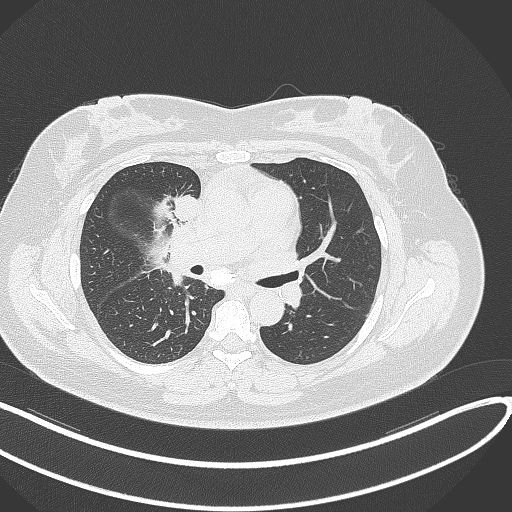
Chest CT, one axial slice. Slice 153 of 303 in the series (ordered by position). Reconstruction kernel B70f. Lung window (W 1500 / L -600 HU). 1 mm slice thickness. 512 × 512 image matrix. Patient: female, 46 years. Case-level facts recorded for this patient, not image findings: clinical TNM (as recorded): T2a N1 M0.
Outlined on this slice (bounding box drawn by a radiologist):
- lung tumour (recorded histology: adenocarcinoma): bounding box <170,194,200,224> (left, top, right, bottom; pixels)